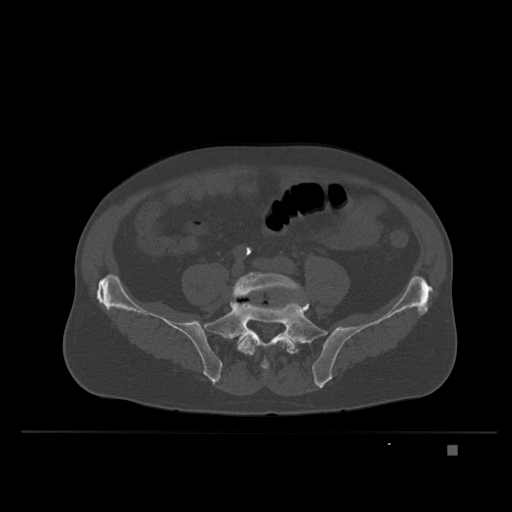
CT including the spine, one axial slice; slice 46 of 435 in the series (ordered by position); bone window (W 1800 / L 400 HU); 1.5 mm slice thickness; 512 × 512 image matrix, field of view 434 × 434 mm. Male patient, age 73 years. From the clinical record (not read from this slice): primary cancer: skin.
Structures marked on this image (semi-automatic segmentation, software-assisted and operator-edited):
- L5 vertebra: bounding box <230,273,303,355> (left, top, right, bottom; pixels)